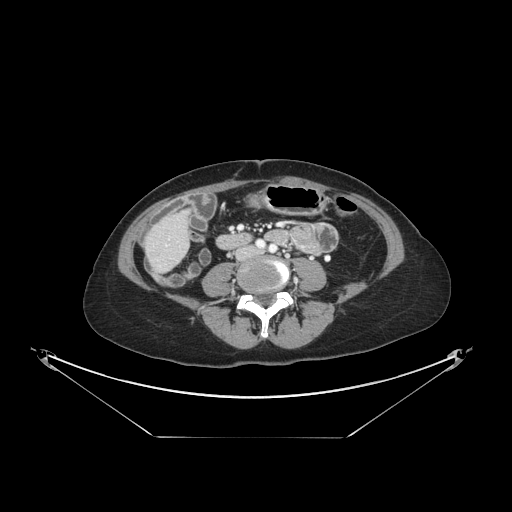
Contrast-enhanced abdominal CT, one axial slice. Slice 26 of 148 in the series (ordered by position). Reconstruction kernel STANDARD. 120 kVp. Soft-tissue window (W 400 / L 40 HU). 2.5 mm slice thickness. 512 × 512 image matrix, field of view 500 × 500 mm. Female patient, age 73 years. Case-level facts recorded for this patient, not image findings: diagnosis: colorectal cancer liver metastases, imaged before liver resection; multiple liver metastases: no; largest metastasis: 1 cm; chemotherapy before resection: yes.
Annotated regions visible in this slice (expert manual segmentation):
- liver: bounding box [x1, y1, x2, y2] px = [150, 214, 187, 269]
- planned liver remnant (the part of the liver to remain after resection): [167, 213, 186, 234]